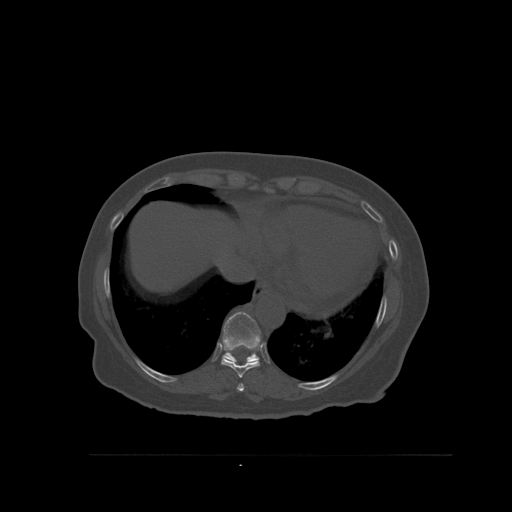
CT including the spine, one axial slice; position 330 of 527 along the scan axis; bone window (W 1800 / L 400 HU); 1.5 mm slice thickness; 512 × 512 image matrix, field of view 470 × 470 mm. Patient: female, 73 years. From the clinical record (not read from this slice): primary cancer: breast.
Structures marked on this image (semi-automatic segmentation, software-assisted and operator-edited):
- T10 vertebra: box from (x=222, y=312) to (x=261, y=363) px
- T8 vertebra: (x=237, y=383)–(x=244, y=392)
- T9 vertebra: (x=221, y=340)–(x=260, y=378)